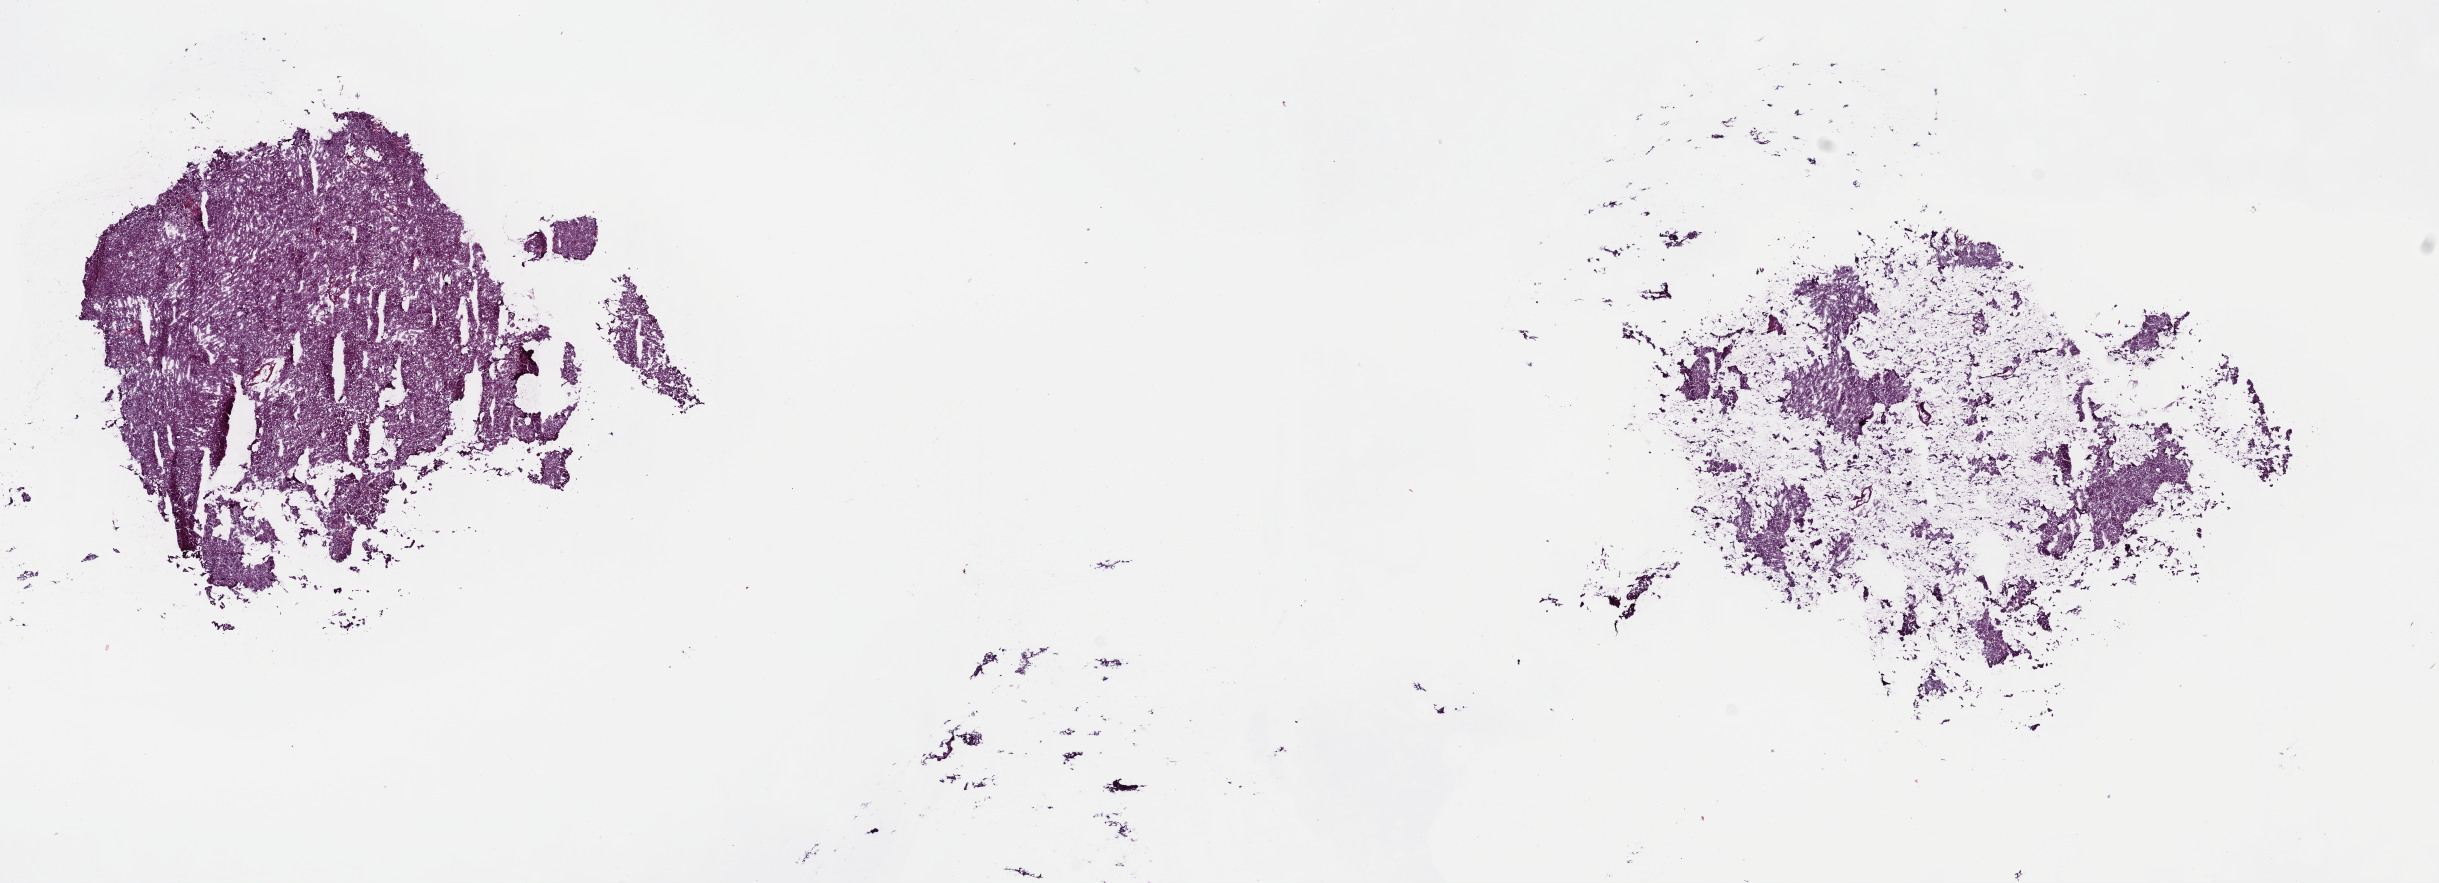
Digitized H&E tissue section (whole slide) — low-resolution overview of the scanned area, about 19.2 x 6.9 mm (from a 40x scan), frozen section, primary tumour sample from the adrenal cortex. Female patient; age at initial diagnosis 57 years. Slide review estimates, as recorded: tumour cells 90%, tumour nuclei 90%, normal cells 0%, stromal cells 10%, necrosis 0%. Inflammatory infiltration, as recorded: lymphocyte infiltration 5%, monocyte infiltration 0%, neutrophil infiltration 0%.
Pathologic diagnosis: Adrenal cortical carcinoma (cortex of adrenal gland).